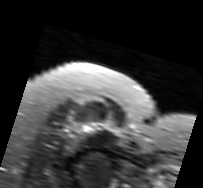
MRI of an extremity soft-tissue mass, one axial slice; position 68 of 91 along the scan axis; T2-weighted fat-saturated; MR volume resampled by the dataset authors to the PET/CT grid (not the native acquisition matrix); 203 × 188 image matrix, field of view 198 × 184 mm. Female patient. Case-level facts recorded for this patient, not image findings: histological type: malignant solitary fibrous tumor; grade: intermediate; site of the primary tumour: right thigh.
Outlined on this slice (expert contour drawn on MRI and transferred to this co-registered scan by the dataset authors):
- gross tumour volume including surrounding oedema: bounding box <63,119,118,148> (left, top, right, bottom; pixels)